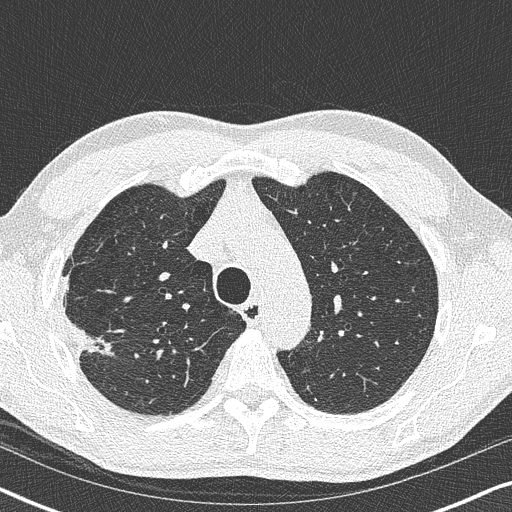
Low-dose screening chest CT, one axial slice; position 277 of 356 along the scan axis; 120 kVp; lung window (W 1500 / L -600 HU); 1 mm slice thickness; 512 × 512 image matrix, field of view 330 × 330 mm.
Structures marked on this image (expert manual segmentation):
- lesion 1 (tumor, upper lobe of right lung): bounding box (x1, y1, x2, y2) in pixels: (72, 324, 114, 356)